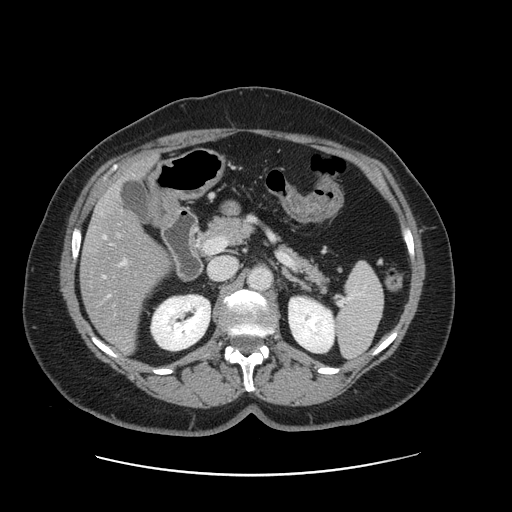
Contrast-enhanced abdominal CT, one axial slice; position 73 of 161 along the scan axis; 120 kVp; intravenous contrast given; soft-tissue window (W 400 / L 40 HU); 512 × 512 image matrix. Female patient, age 62 years. From the clinical record (not read from this slice): diagnosis: colorectal cancer liver metastases, imaged before liver resection; multiple liver metastases: no; largest metastasis: 2.5 cm; disease in both lobes: no.
Outlined on this slice (manually delineated by an expert):
- hepatic veins: box from (x=103, y=235) to (x=110, y=297) px
- liver: (x=82, y=160)–(x=169, y=352)
- planned liver remnant (the part of the liver to remain after resection): (x=124, y=161)–(x=151, y=180)
- portal vein (with intrahepatic branches): (x=118, y=235)–(x=125, y=265)